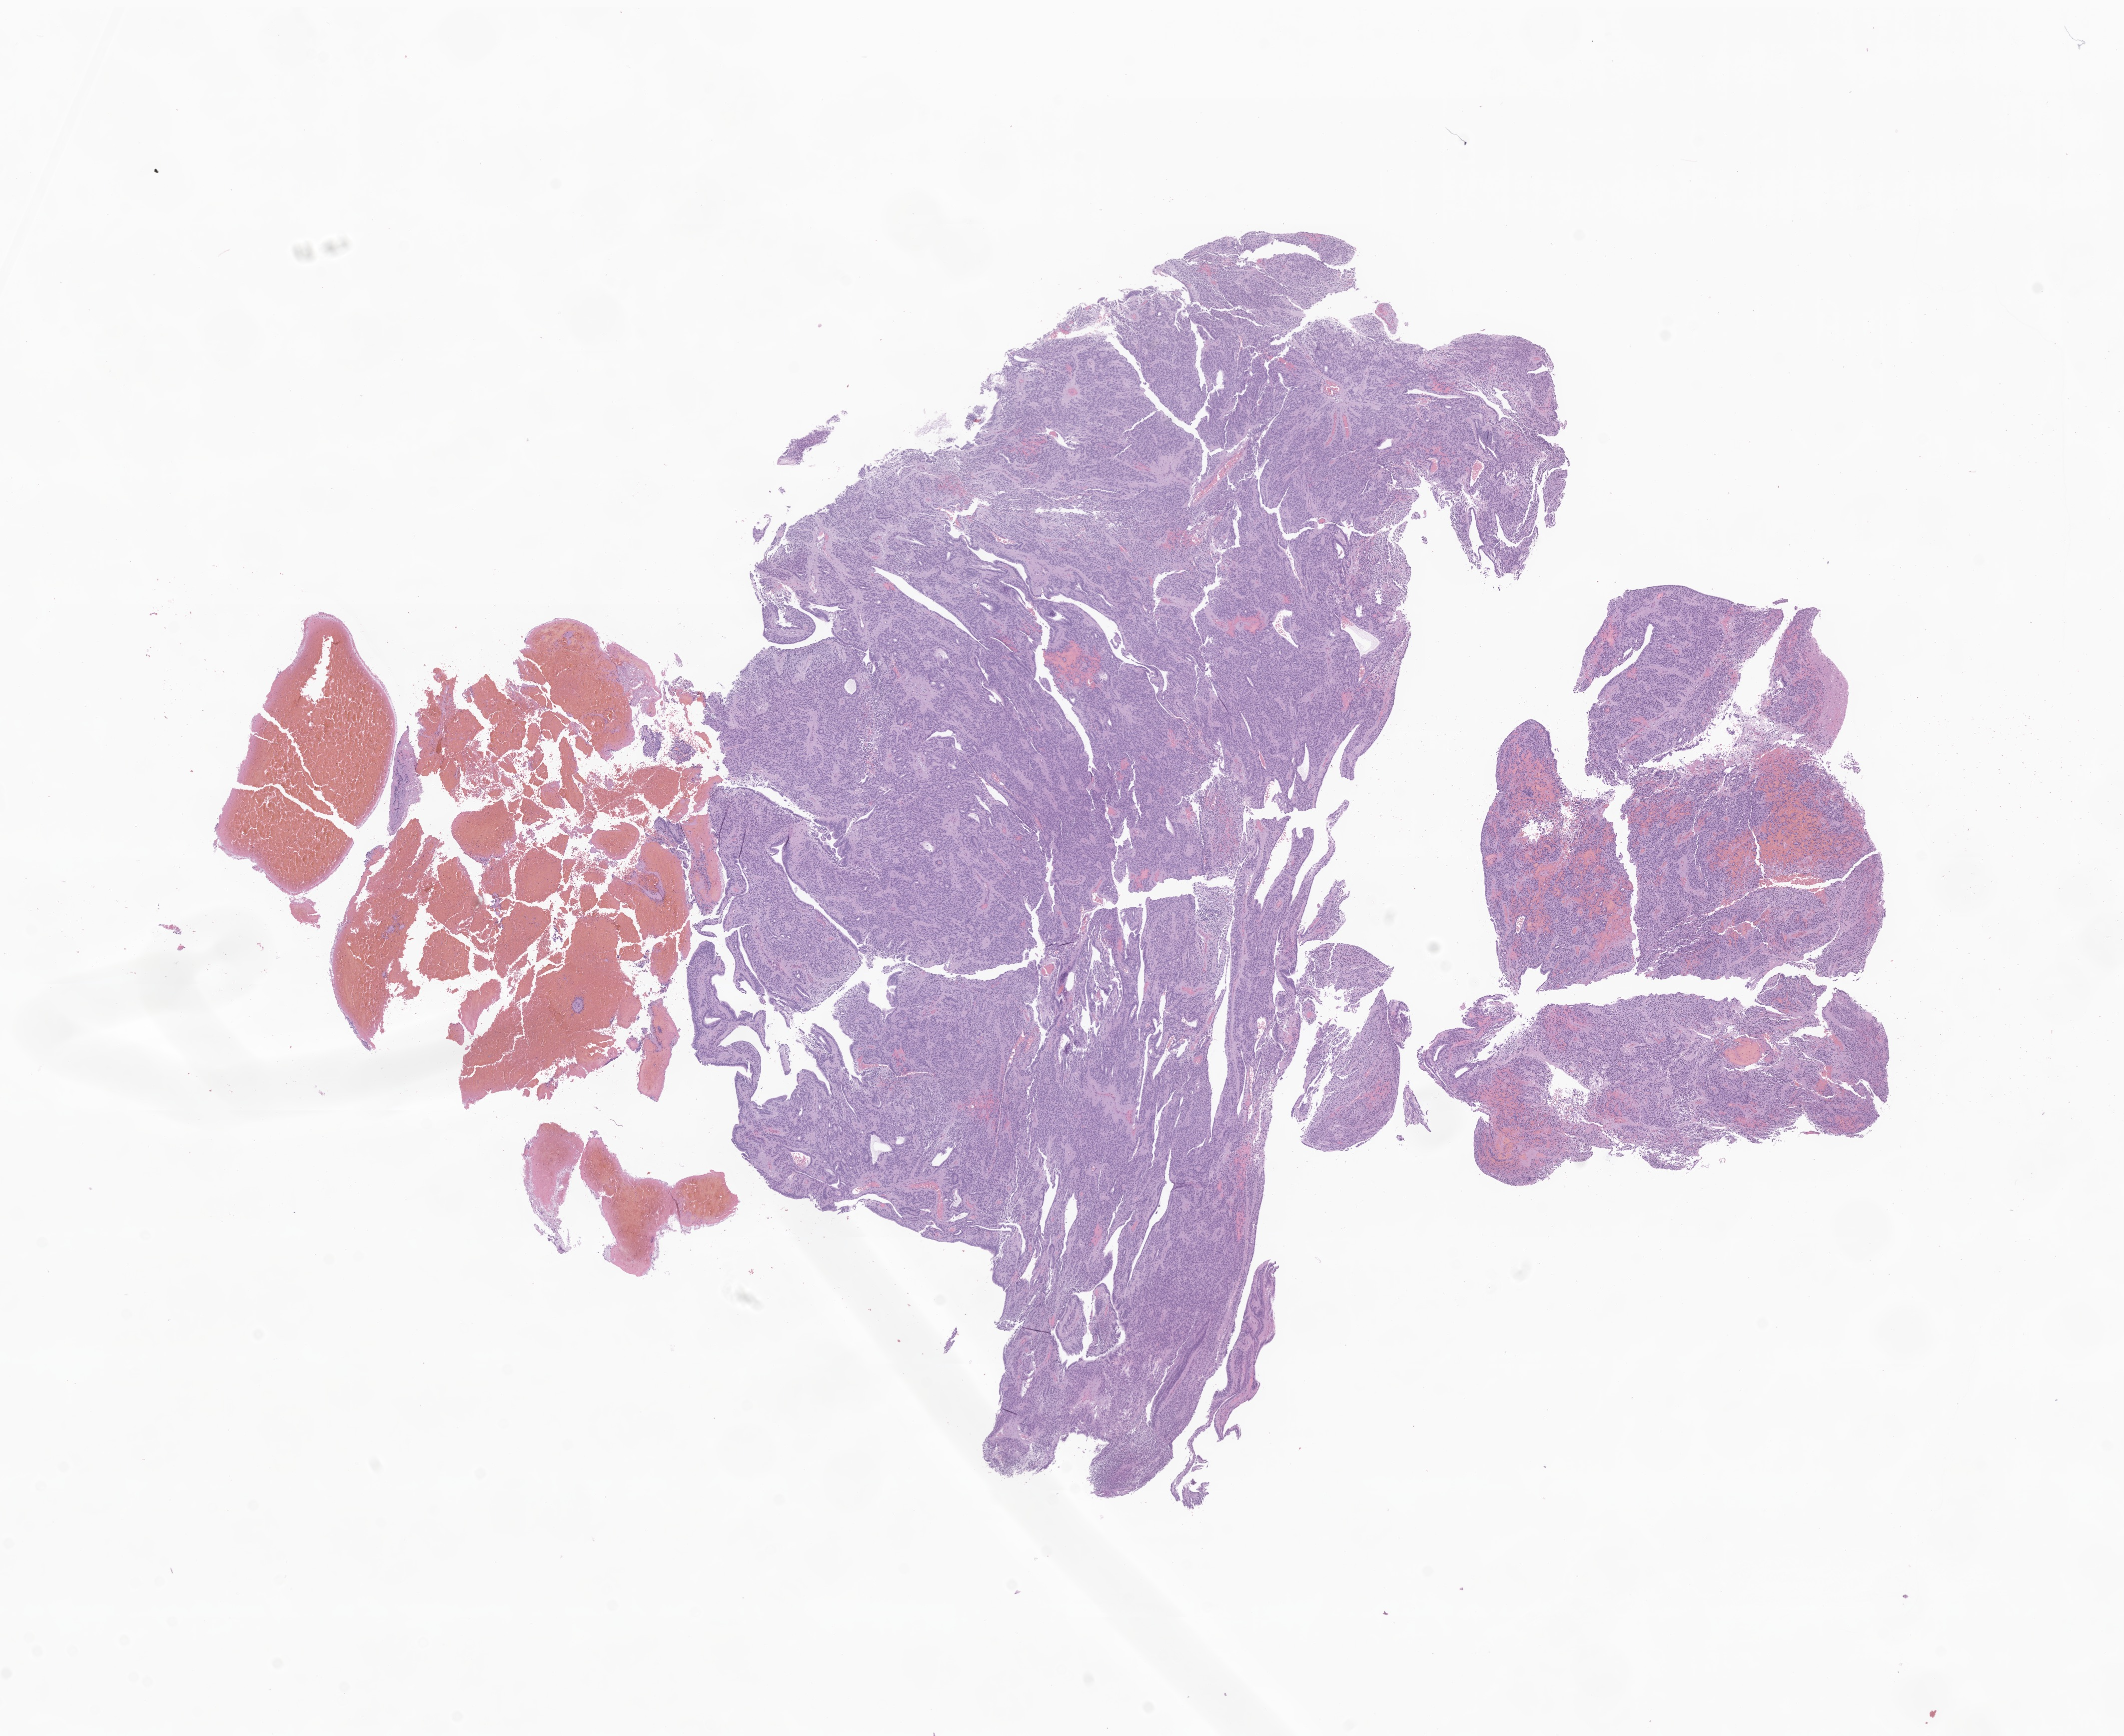
Digitized hematoxylin and eosin (H&E)-stained section of tumor tissue from the spinal cord, a low-resolution overview of the entire scanned area, about 17.9 x 14.6 mm, formalin-fixed, paraffin-embedded (FFPE) tissue. Patient: female, age 184 months (15 years 4 months).
* diagnosis: Astrocytoma, NOS